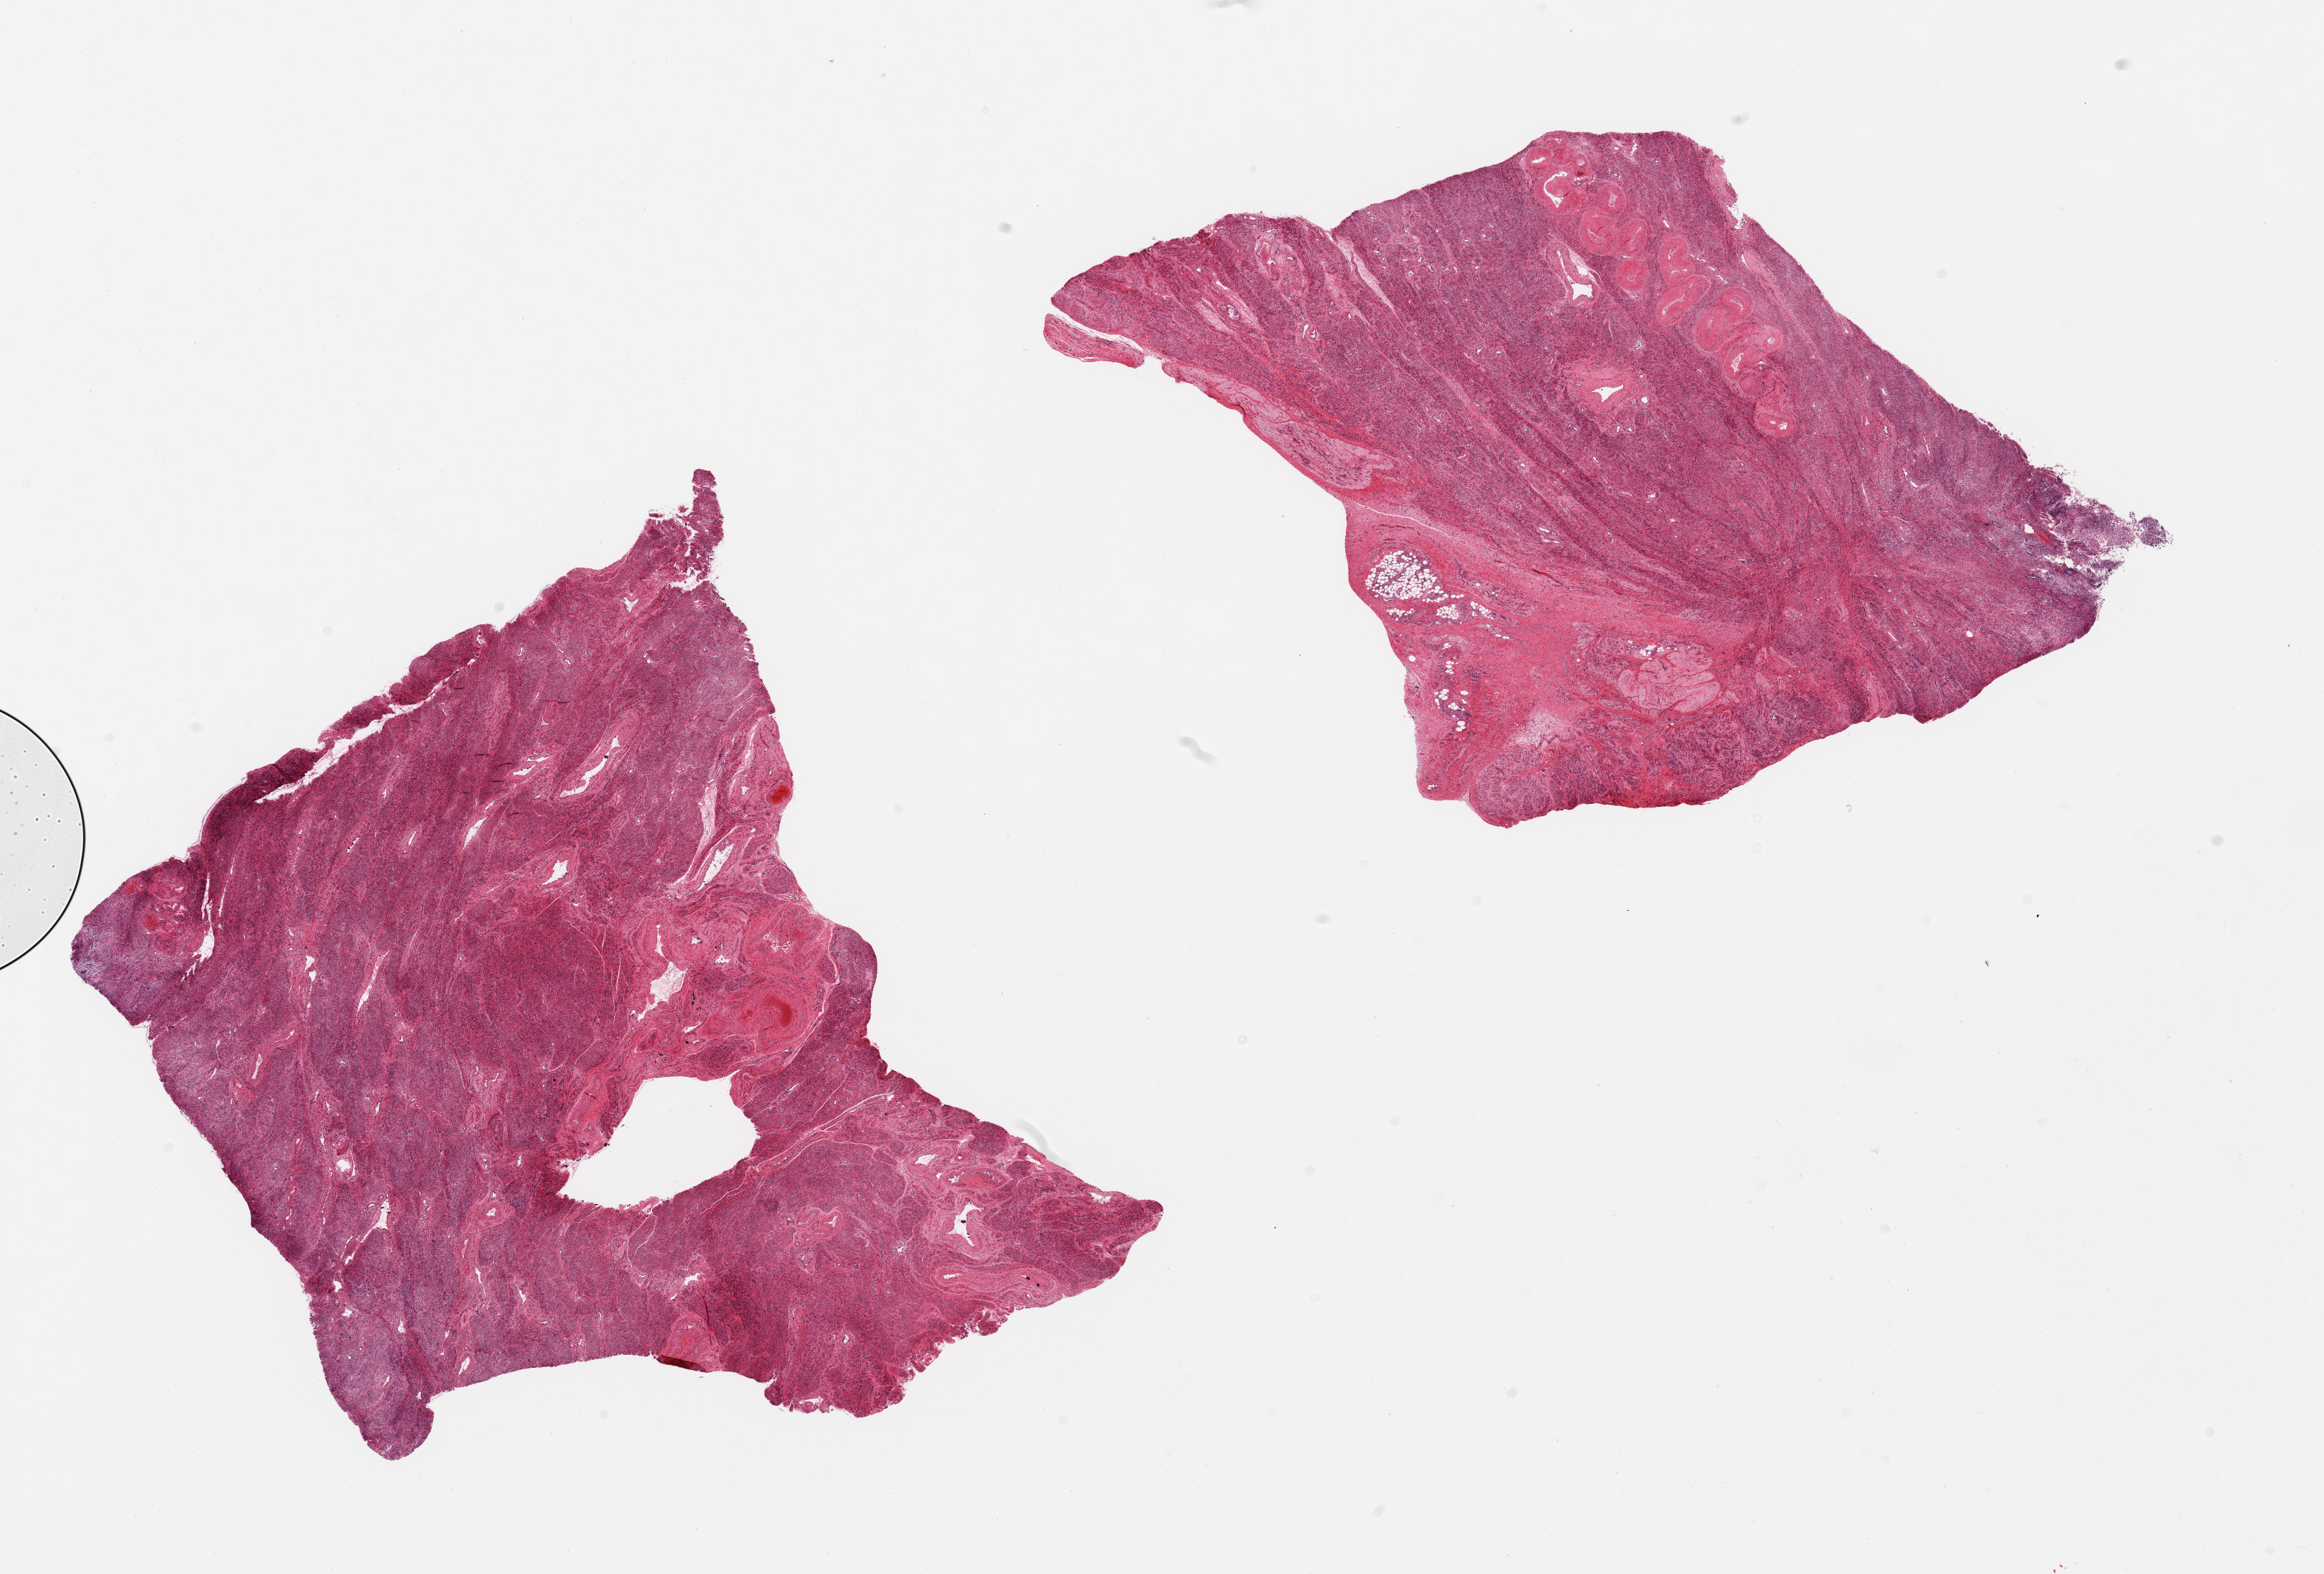
Hematoxylin and eosin (H&E) whole-slide image, shown as a low-resolution overview of the whole scanned area (about 25.6 x 17.3 mm). PAXgene-fixed, paraffin-embedded tissue. Target tissue: uterus. Tissue donor sample. Donor: female.
- review note (as recorded): 2 pieces; only myometrium, no endometrium